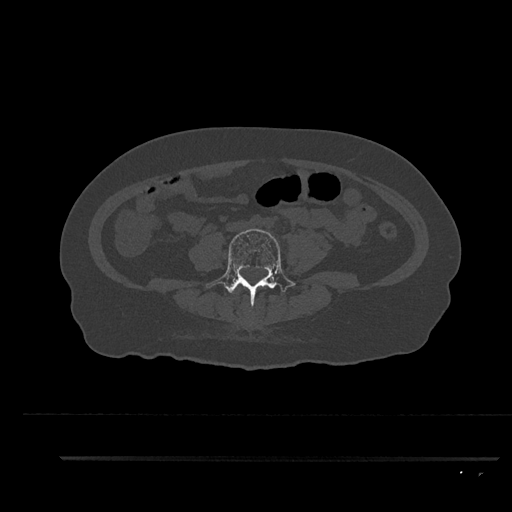
CT including the spine, one axial slice; slice 28 of 797 in the series (ordered by position); 120 kVp; bone window (W 1800 / L 400 HU); 512 × 512 image matrix. Patient: female, 44 years. From the clinical record (not read from this slice): primary cancer: renal; vertebrae with lytic lesions (as recorded): L1.
Outlined on this slice (semi-automatic segmentation, software-assisted and operator-edited):
- L4 vertebra: bounding box [x1, y1, x2, y2] px = [206, 229, 296, 311]